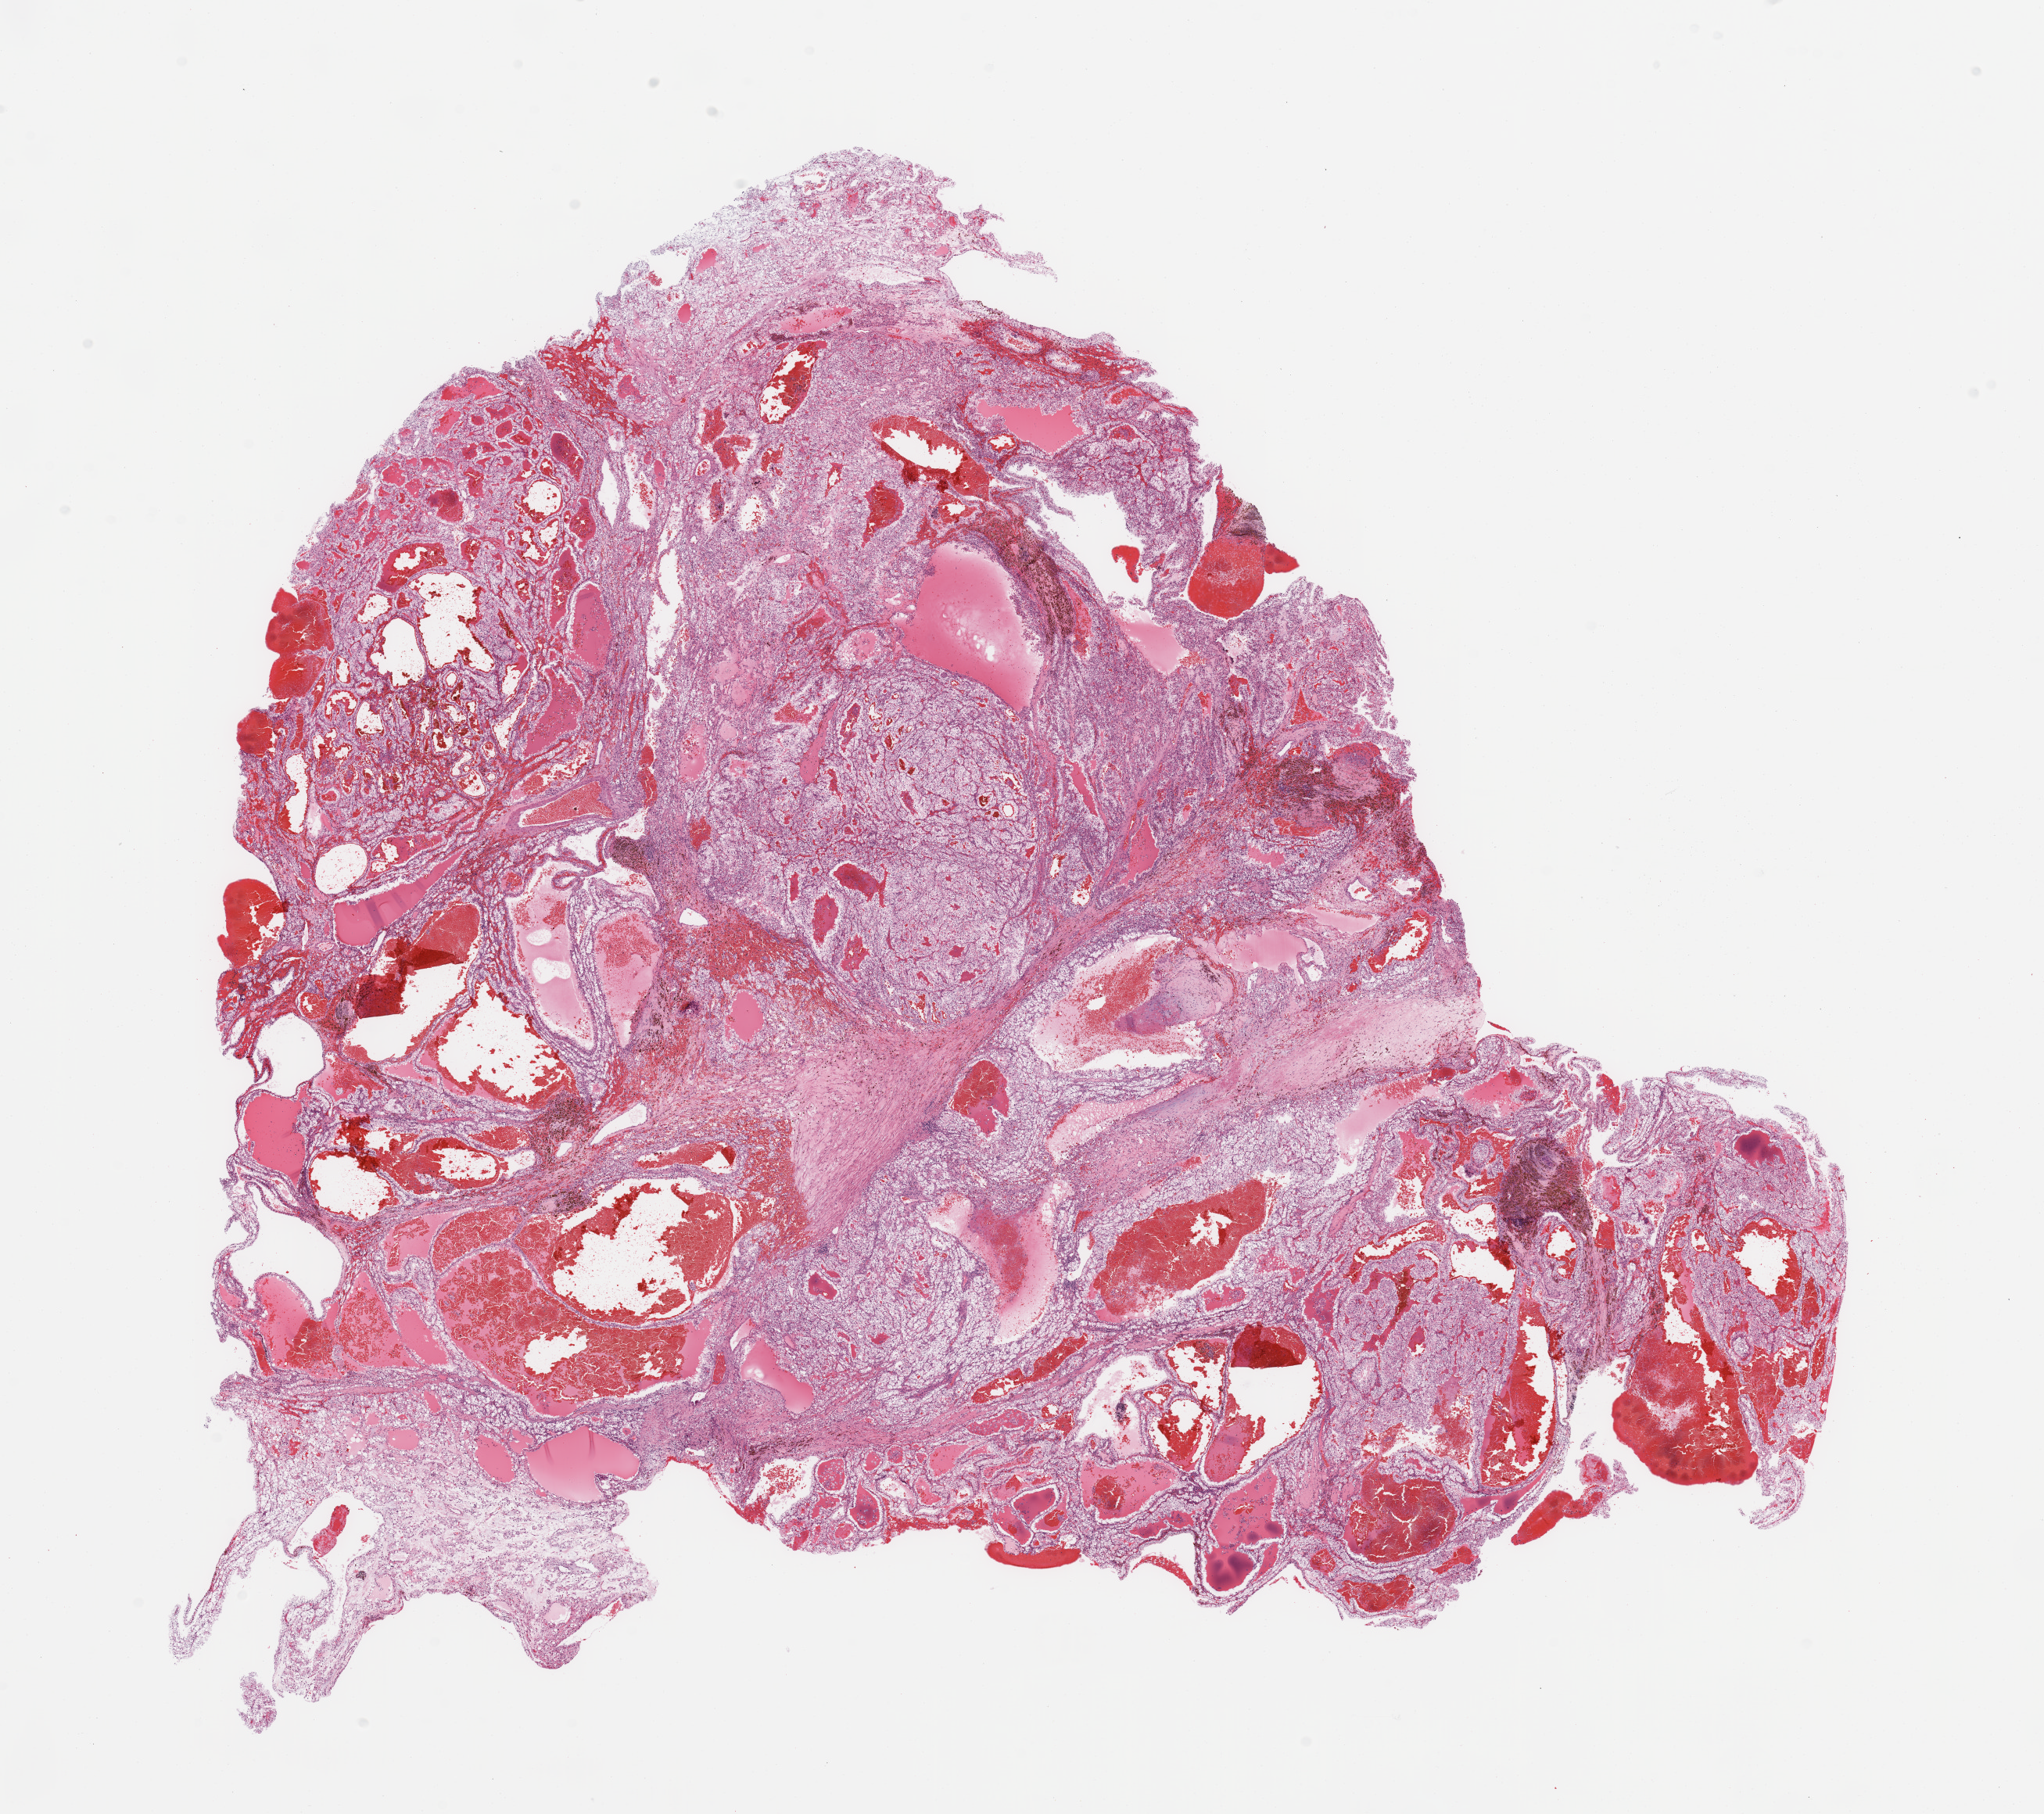
H&E-stained whole-slide image — whole scanned area (about 20.7 x 18.3 mm, from a 20x scan) shown as a low-resolution overview, tumour tissue sample, sampled site: kidney. 55-year-old male patient. Histologic grade: G2 (moderately differentiated). Composition of this section per pathologist review: tumour nuclei 90%, necrosis 0%.
• diagnosis: Renal cell carcinoma, NOS
• AJCC pathologic stage: I
• primary tumour site (as recorded): lower pole